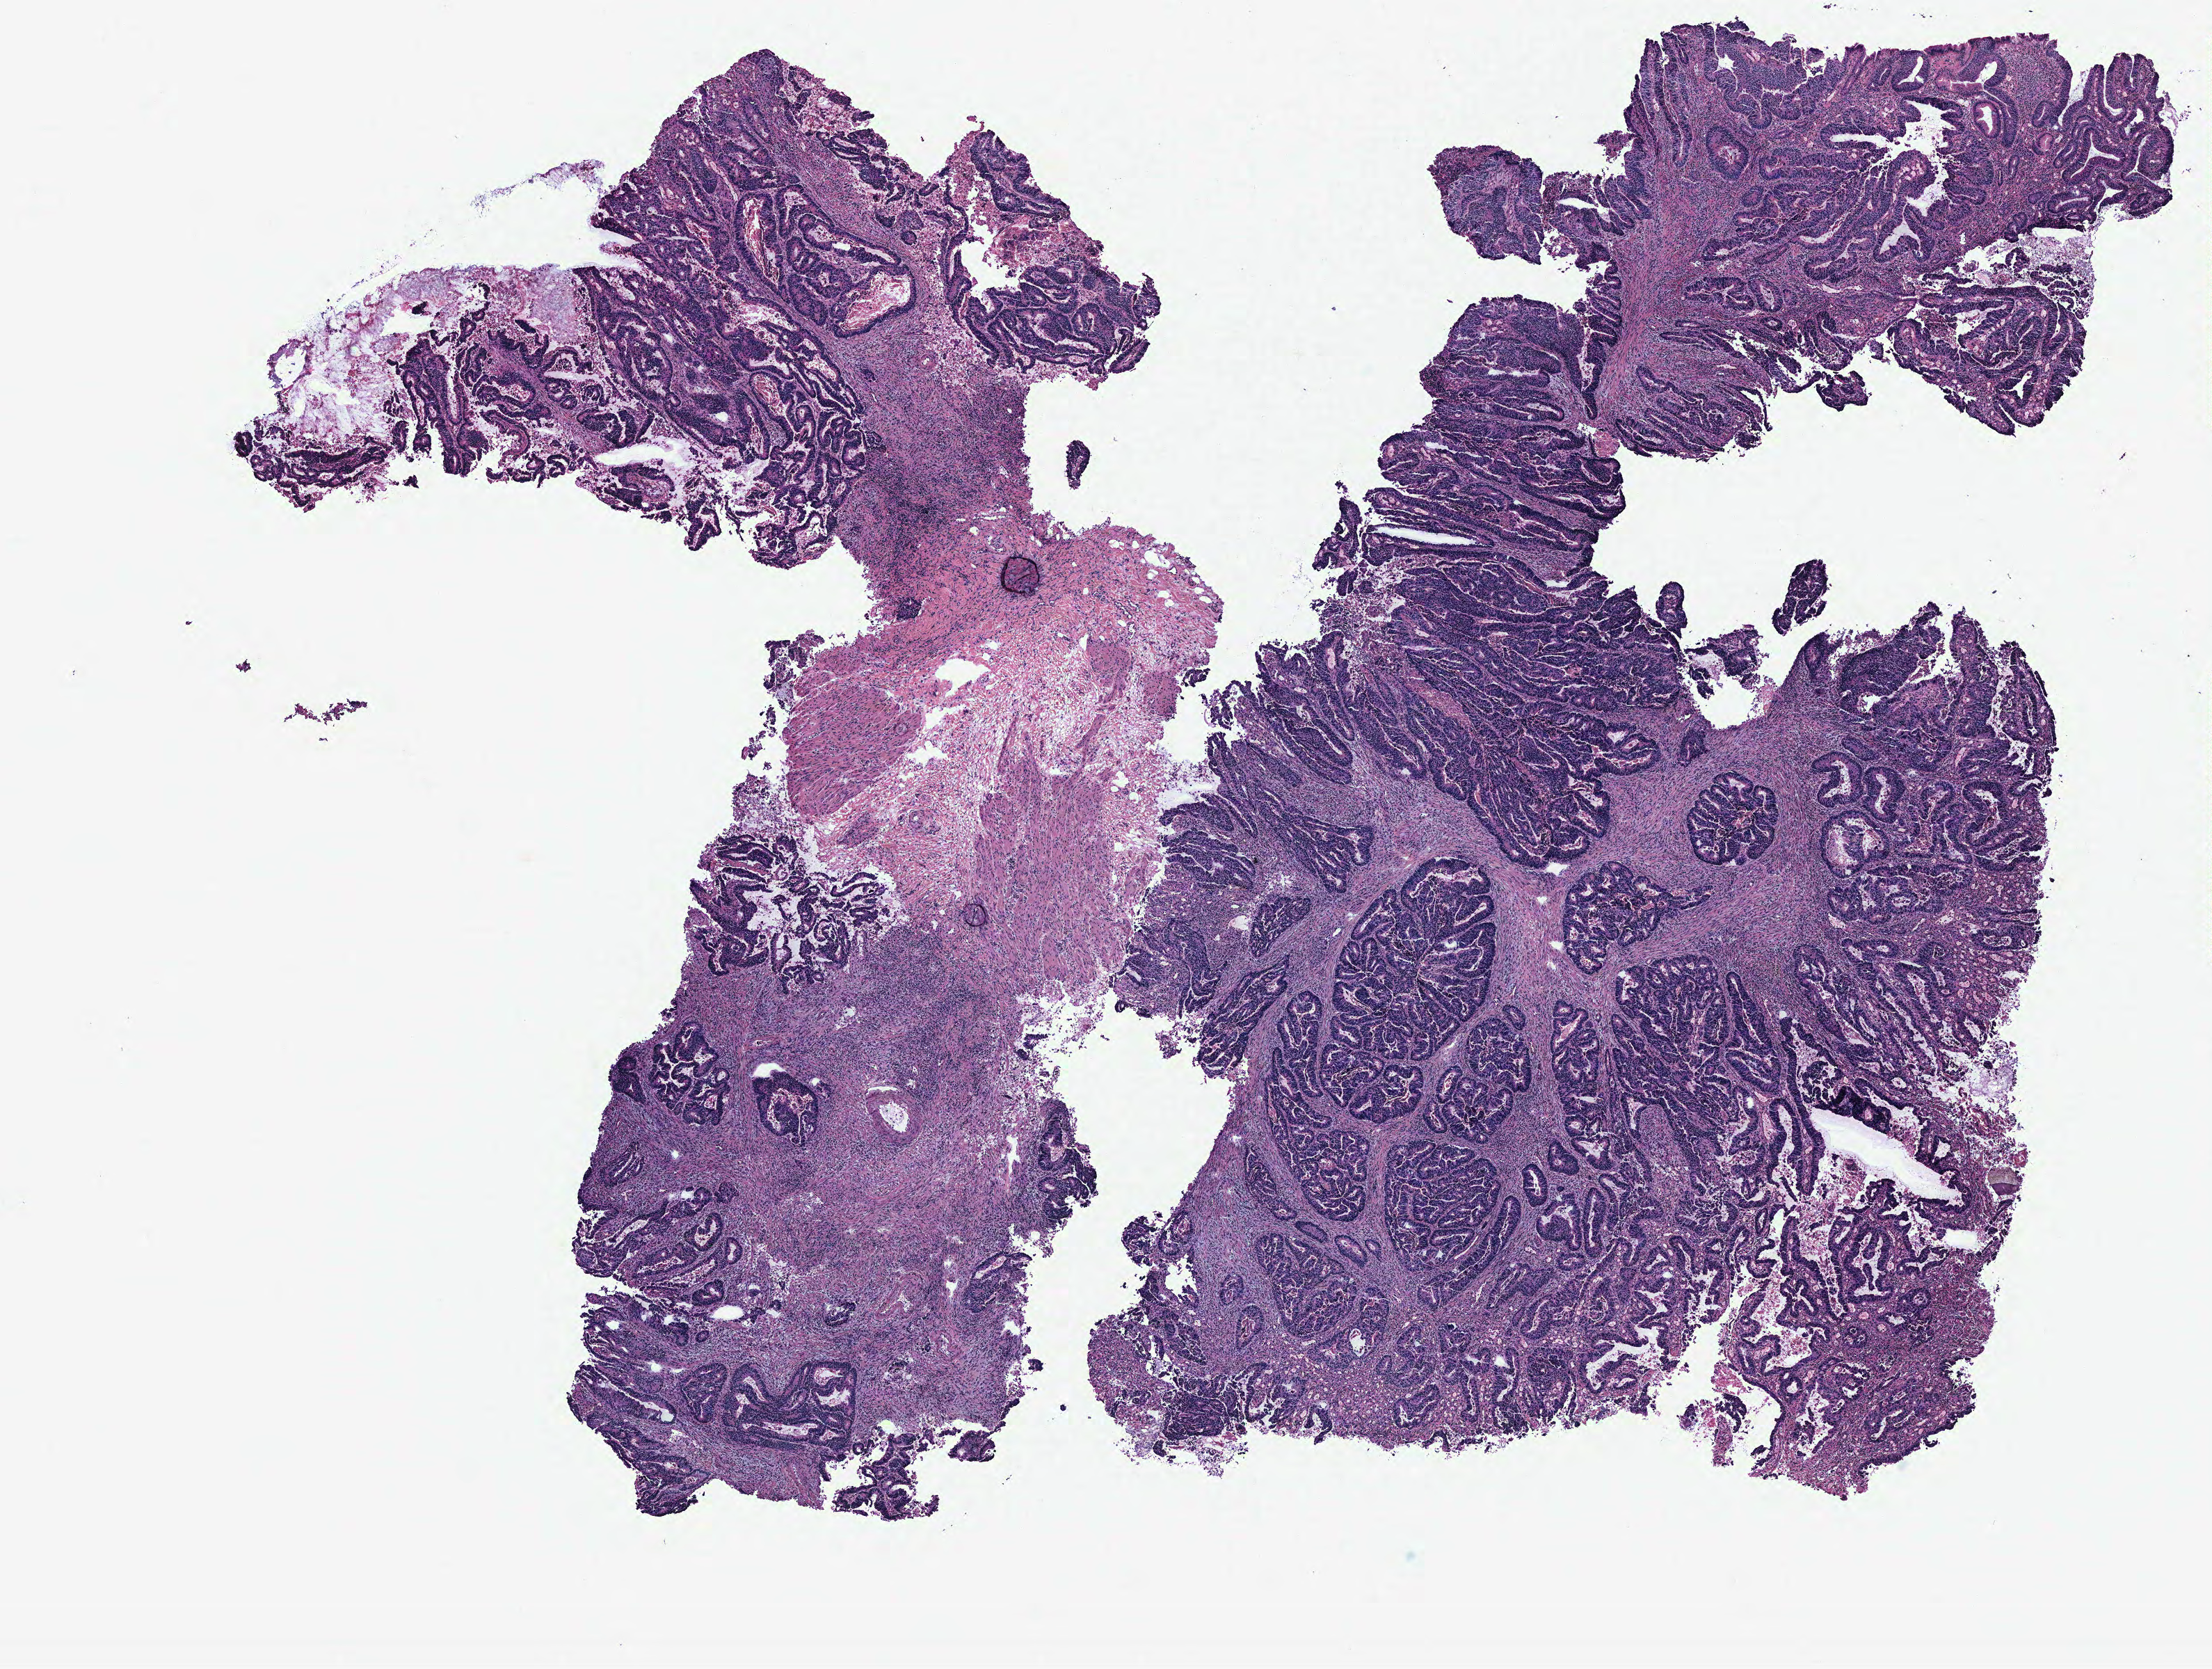
Whole-slide histology image, H&E-stained — shown as a low-resolution overview of the whole scanned area (about 12.7 x 9.6 mm, slide scanned at 40x). Normal (non-tumour) tissue sample, colon. Patient: male, age 88 years.
• this section: normal (non-tumour) tissue from the same patient
• patient diagnosis: Adenocarcinoma, NOS